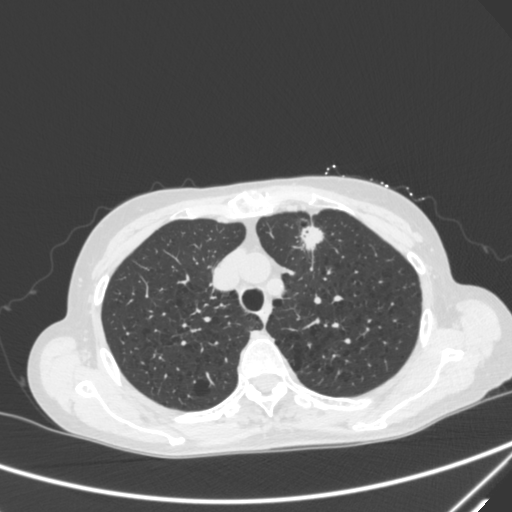
Chest CT, one axial slice. Lung window (W 1500 / L -600 HU). 1 mm slice thickness. 512 × 512 image matrix, field of view 350 × 350 mm. Female patient, age 71 years. Case-level facts recorded for this patient, not image findings: clinical TNM (as recorded): T1c N0 M0; histopathological grade: G2-3.
Outlined on this slice (bounding box drawn by a radiologist):
- lung tumour (recorded histology: adenocarcinoma): bounding box [x1, y1, x2, y2] px = [293, 220, 332, 256]